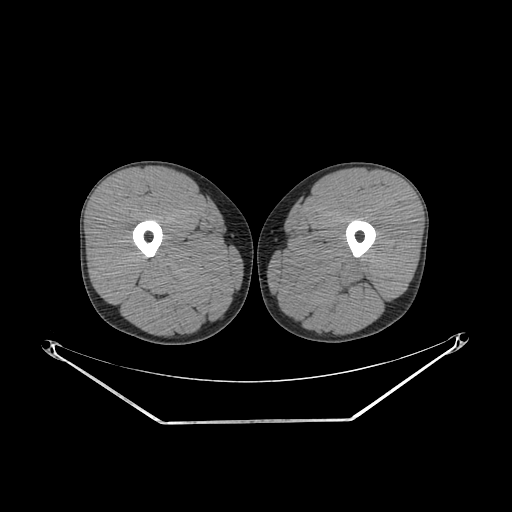
CT of an extremity soft-tissue mass (from a PET/CT study), one axial slice; slice 231 of 267 in the series (ordered by position); 140 kVp; soft-tissue window (W 400 / L 40 HU); 512 × 512 image matrix, field of view 500 × 500 mm. Male patient. Case-level facts recorded for this patient, not image findings: histological type: extraskeletal osteosarcoma; grade: high; site of the primary tumour: left adductur.
Structures marked on this image (expert contour drawn on MRI and transferred to this co-registered scan by the dataset authors):
- gross tumour volume (mass): bounding box [x1, y1, x2, y2] px = [270, 244, 371, 312]